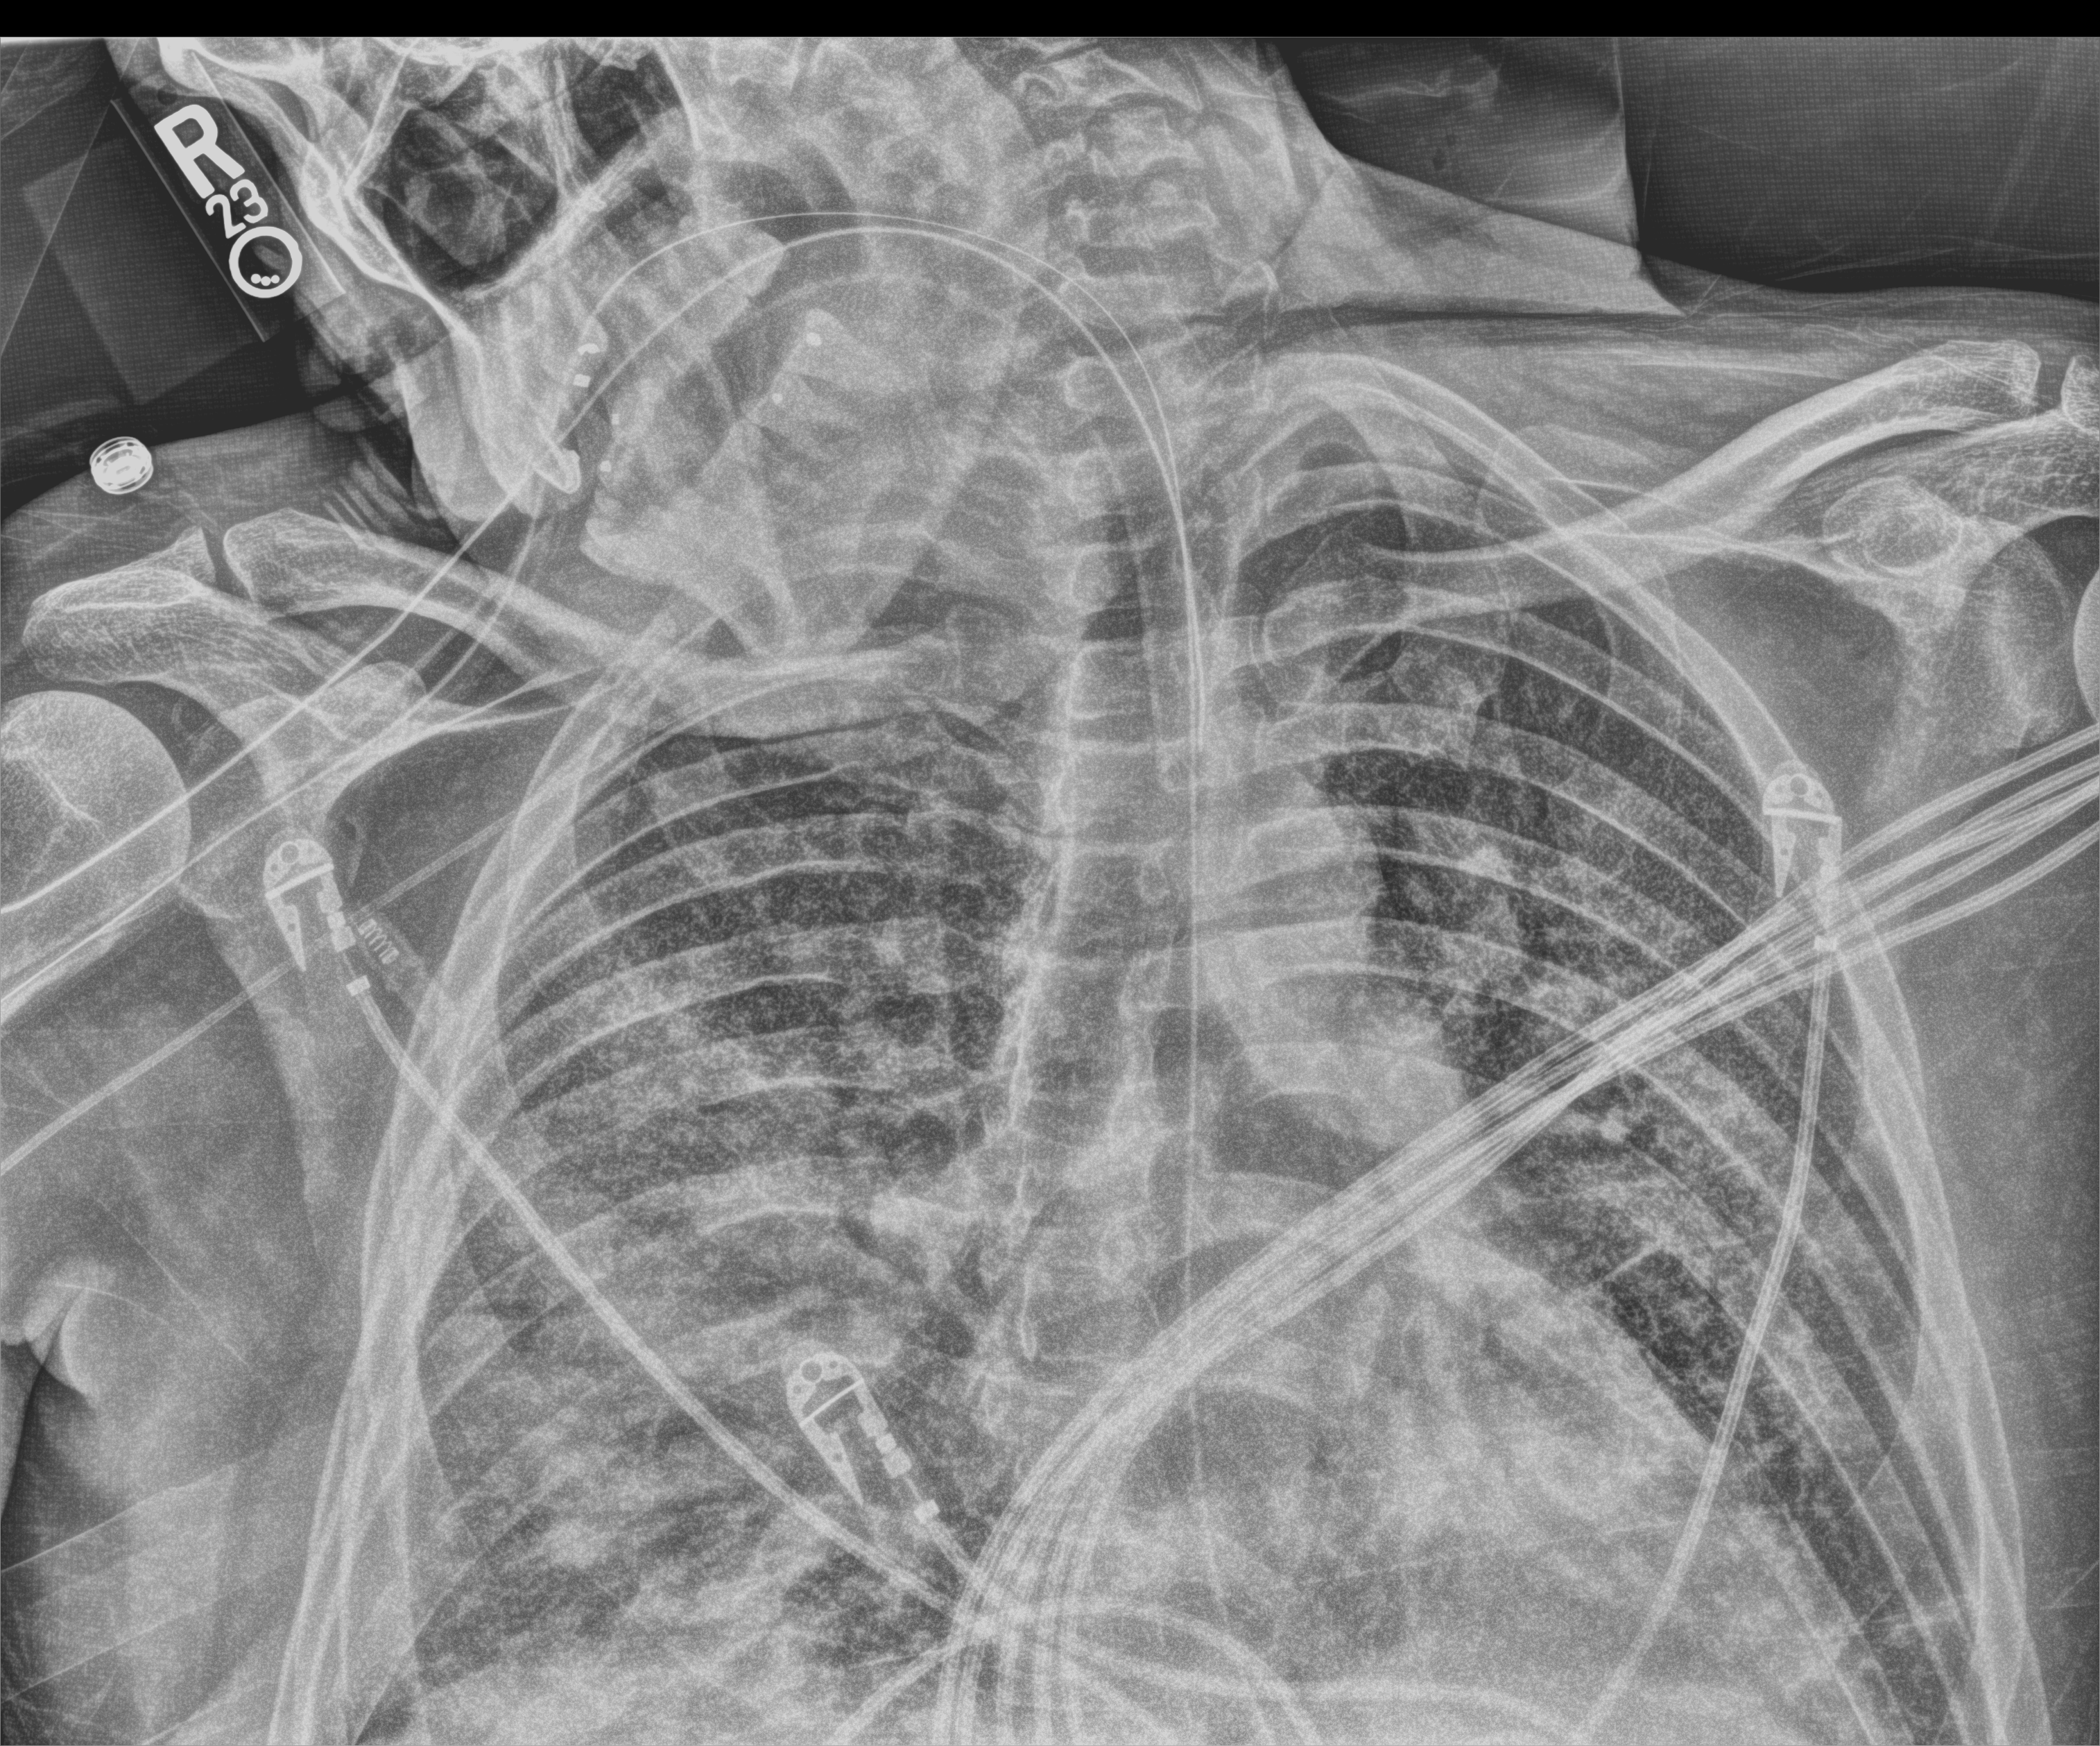
Portable chest radiograph, anteroposterior (AP) projection. Male patient hospitalised with COVID-19, age 18–59 years.
Admission-level facts for this patient (not findings on this image; timing relative to this image not recorded): mechanically ventilated during this hospital stay: yes.